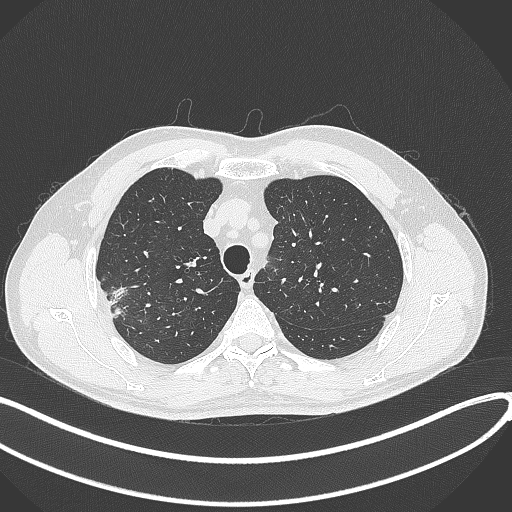
Chest CT, one axial slice. Position 331 of 381 along the scan axis. Reconstruction kernel B70f. 120 kVp. Lung window (W 1500 / L -600 HU). 1 mm slice thickness. 512 × 512 image matrix, field of view 400 × 400 mm. Male patient, age 62 years. Case-level facts recorded for this patient, not image findings: clinical TNM (as recorded): T1c N0 M0; histopathological grade: G2-3.
Structures marked on this image (bounding box drawn by a radiologist):
- lung tumour (recorded histology: adenocarcinoma): bounding box <106,279,131,324> (left, top, right, bottom; pixels)